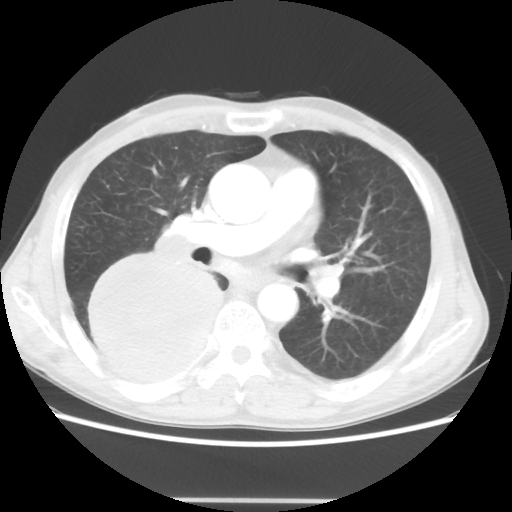
Chest CT, one axial slice. Position 26 of 48 along the scan axis. Reconstruction kernel STANDARD. 100 kVp. Lung window (W 1500 / L -600 HU). 512 × 512 image matrix. Patient: male, 66 years. From the clinical record (not read from this slice): clinical TNM (as recorded): T4 N1 M1; histopathological grade: G3.
Outlined on this slice (bounding box drawn by a radiologist):
- lung tumour (recorded histology: small cell carcinoma): box from (x=80, y=242) to (x=225, y=395) px